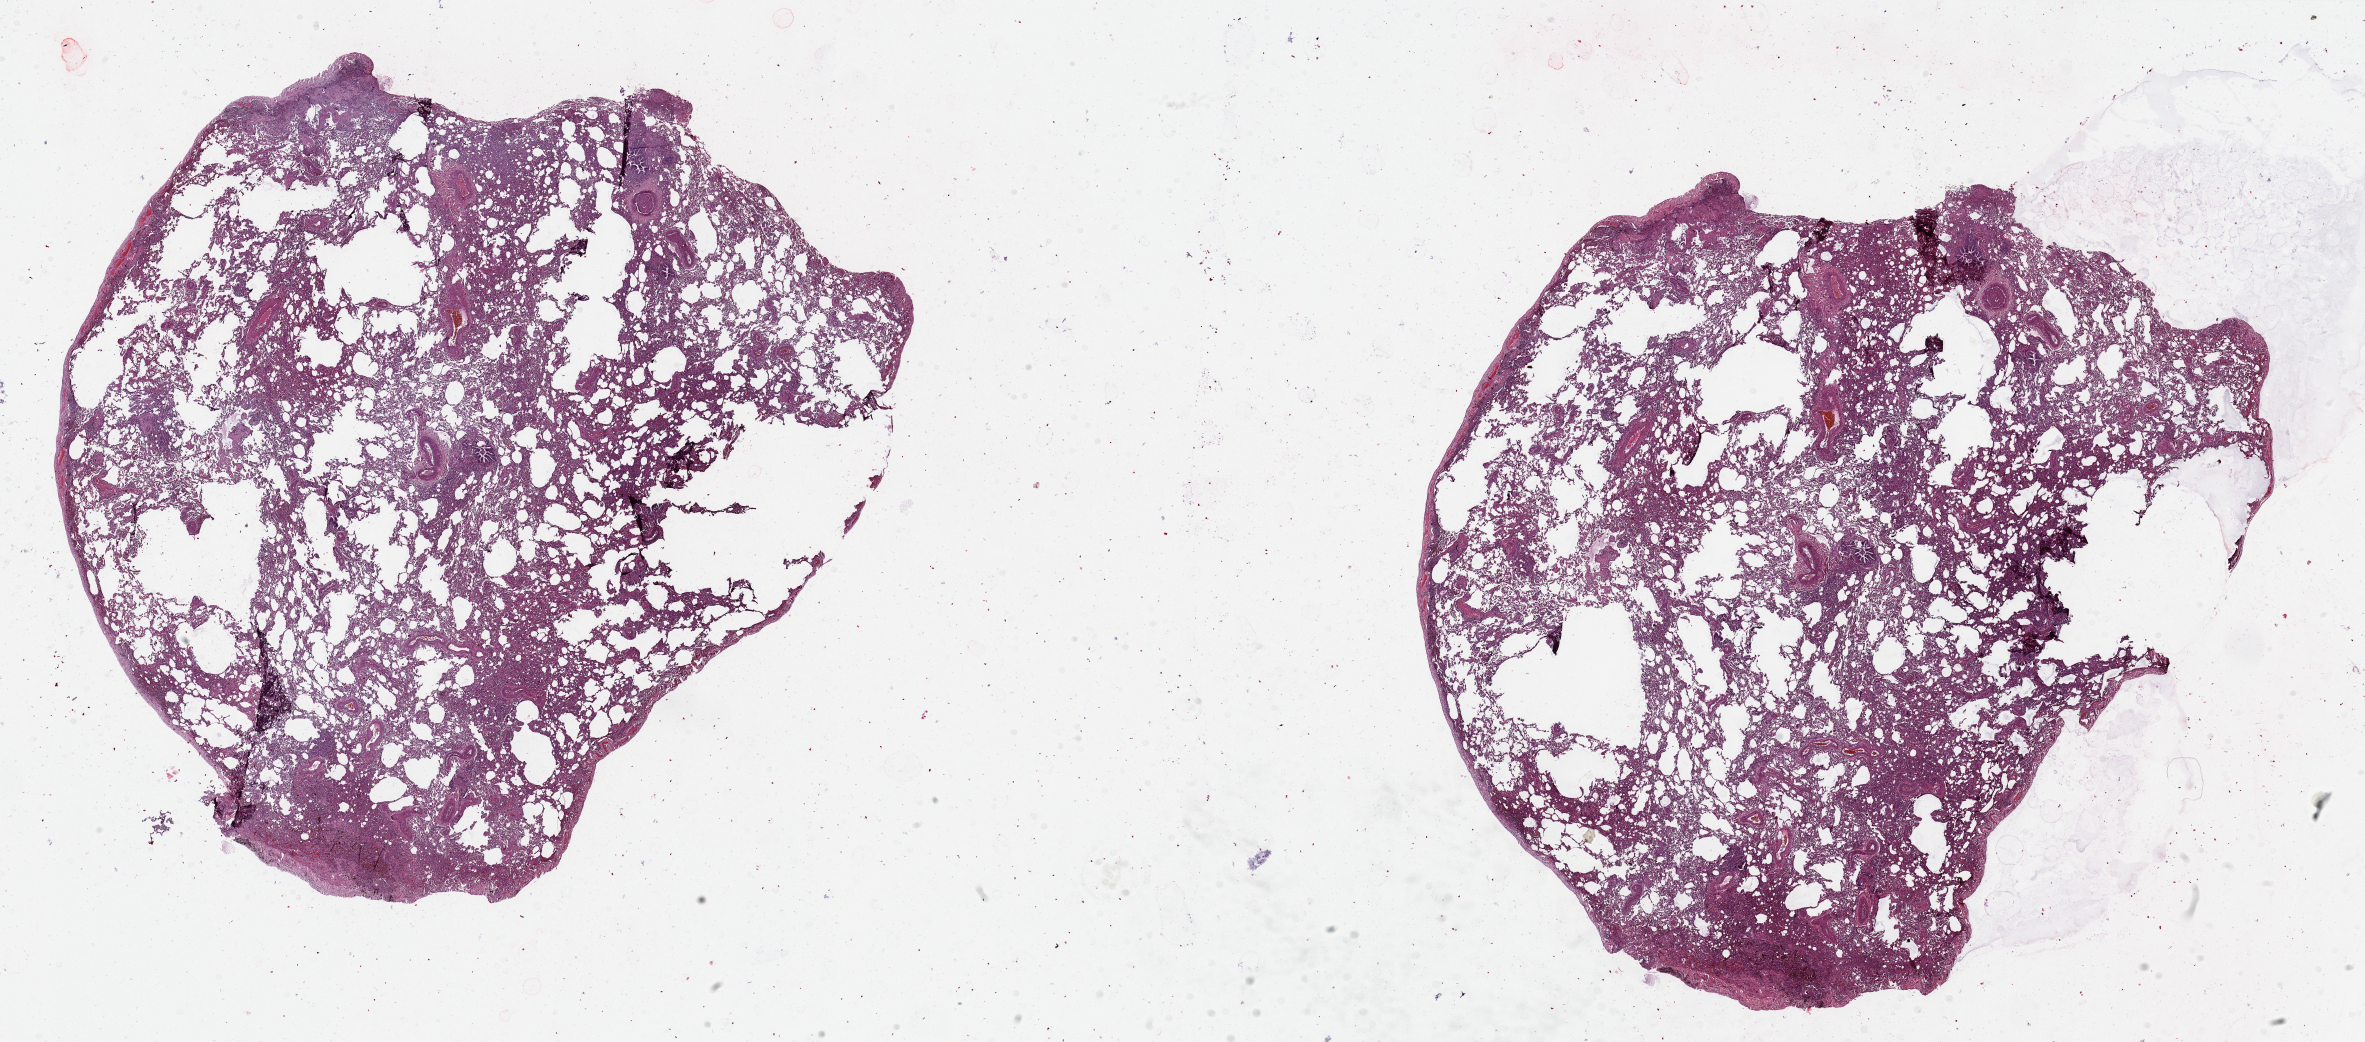
Digitized H&E-stained tissue section (whole slide) — whole scanned area (about 37.4 x 16.5 mm, slide scanned at 20x) shown as a low-resolution overview. Normal (non-tumour) tissue sample, lung. Male, 57 y/o.
This section: normal (non-tumour) tissue from the same patient. Patient diagnosis: Squamous cell carcinoma, NOS.